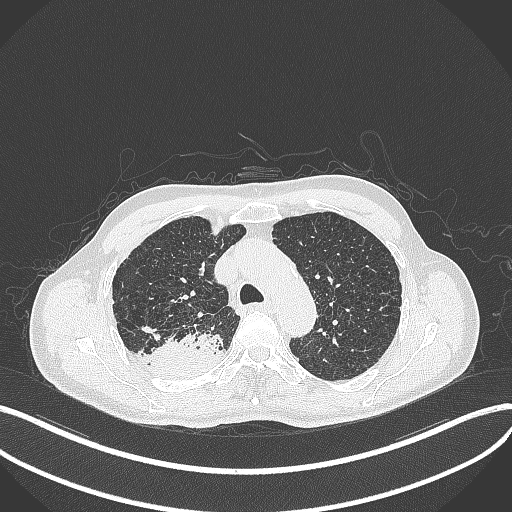
Chest CT, one axial slice; slice 330 of 428 in the series (ordered by position); lung window (W 1500 / L -600 HU); 512 × 512 image matrix, field of view 400 × 400 mm. Patient: male, 79 years. Case-level facts recorded for this patient, not image findings: clinical TNM (as recorded): T3 N0 M0.
Structures marked on this image (bounding box drawn by a radiologist):
- lung tumour (recorded histology: adenocarcinoma): bounding box <146,331,222,381> (left, top, right, bottom; pixels)